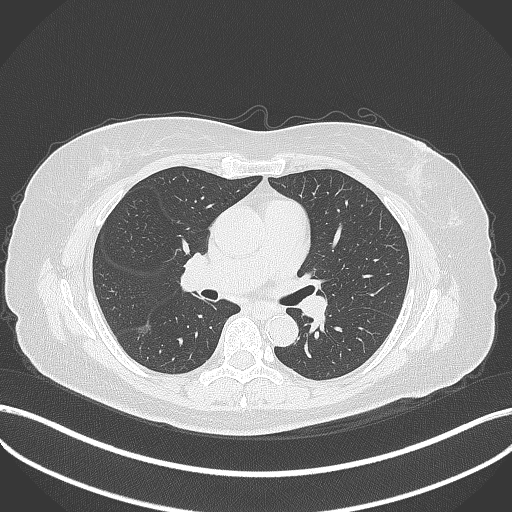
Chest CT, one axial slice. Position 180 of 322 along the scan axis. 120 kVp. Lung window (W 1500 / L -600 HU). 1 mm slice thickness. 512 × 512 image matrix, field of view 400 × 400 mm. Patient: female, 64 years. From the clinical record (not read from this slice): clinical TNM (as recorded): T1c N0 M0; histopathological grade: G1.
Outlined on this slice (rectangle marked by the reading radiologist):
- lung tumour (recorded histology: adenocarcinoma): bounding box (x1, y1, x2, y2) in pixels: (134, 322, 156, 338)